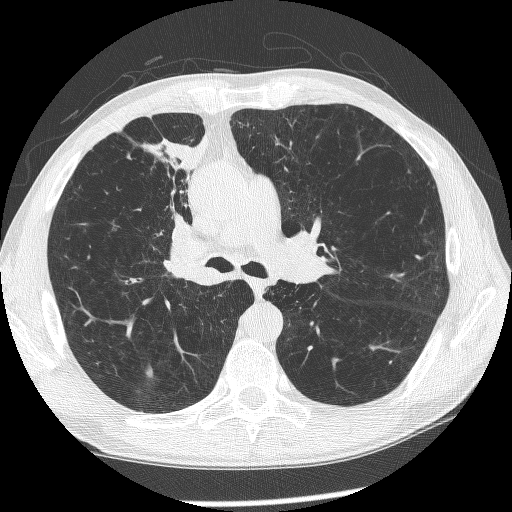
Chest CT (low-dose screening protocol), one axial image. Baseline annual screen. Lung window (W 1500 / L -600 HU). 1.25 mm slice thickness. Lung (sharp) reconstruction kernel (BONE). Slice 149 of 266 in the series. Male, age 60 years at enrolment. Current smoker at enrolment.
Expert-annotated lung lesion, bounding box (x1, y1, x2, y2) in pixels: (145, 196, 222, 289). The exam's reader record, not a measurement of the box and not confirmed to be the same lesion: non-calcified nodule or mass ≥4 mm, right upper lobe, 12 × 8 mm, spiculated (stellate) margins, mixed attenuation. Later outcome: lung cancer diagnosed 208 days after this screen — squamous cell carcinoma, NOS, right upper lobe, right middle lobe, right main stem bronchus, poorly differentiated (G3), stage IV (AJCC 6th edition).